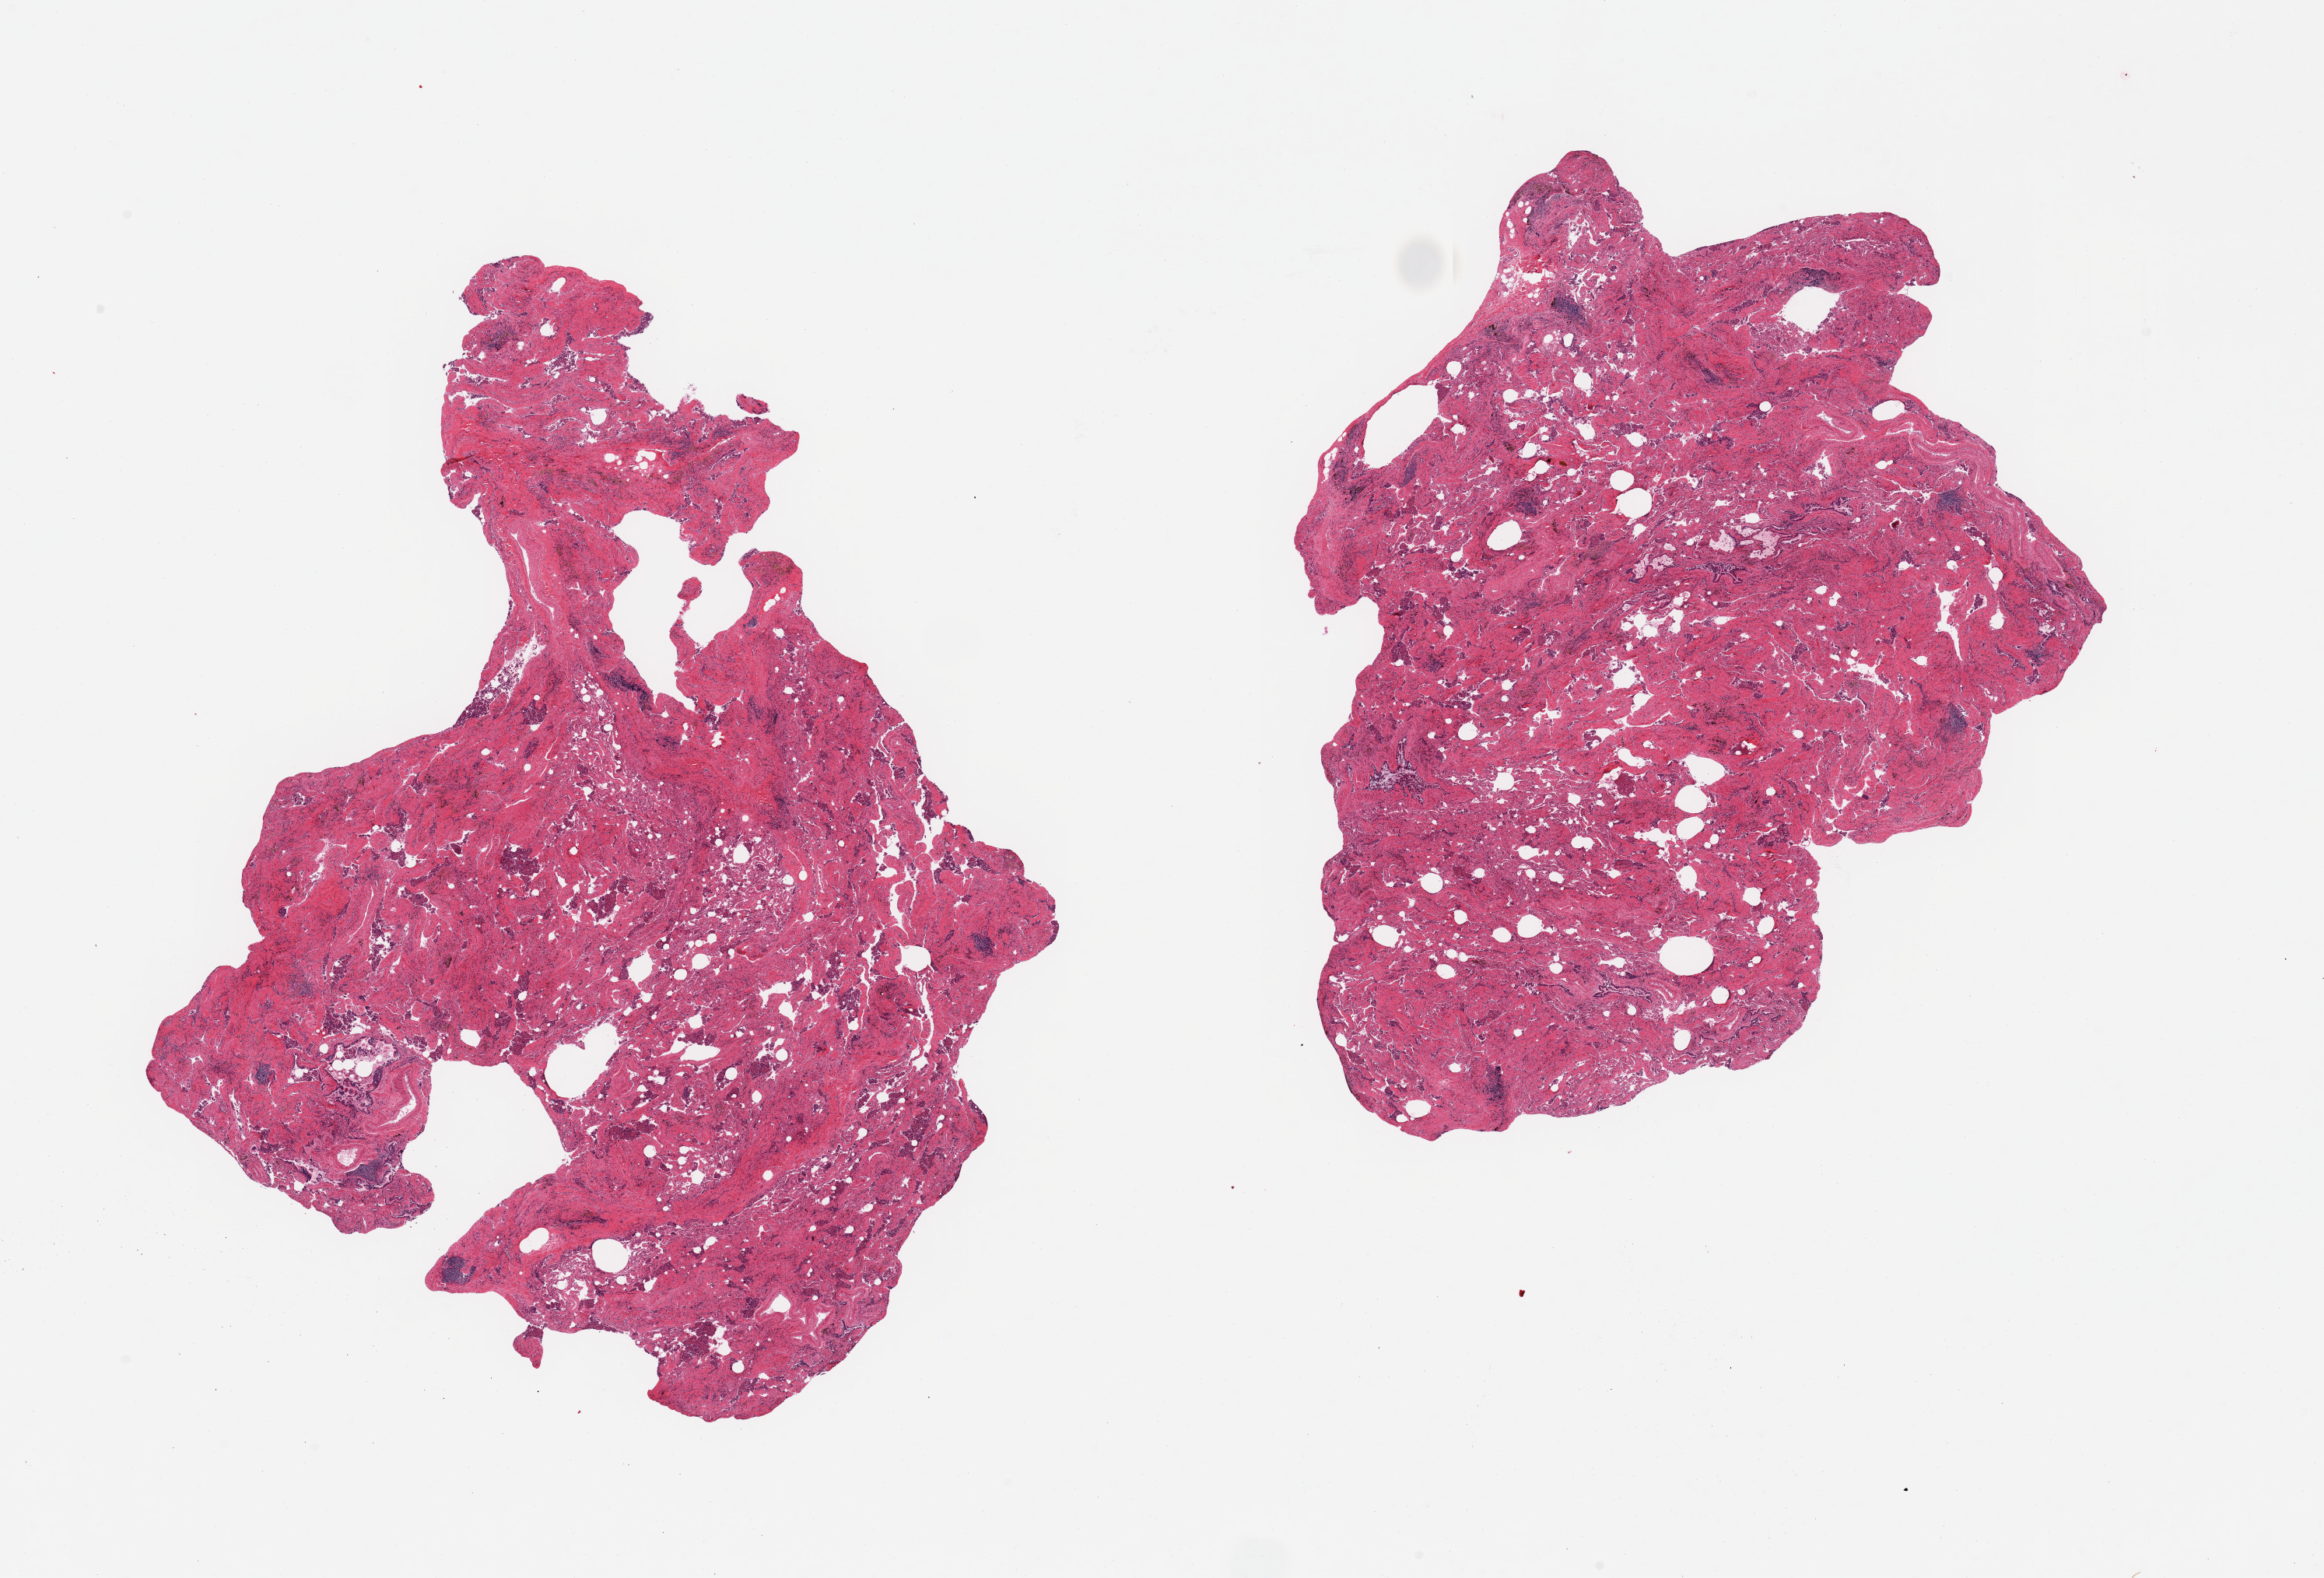
Hematoxylin and eosin (H&E) whole-slide image, a low-resolution overview of the entire scanned area, about 23.6 x 16.0 mm; PAXgene-fixed, paraffin-embedded tissue; sampled site (target tissue): lung; donor tissue sample. Donor: male.
Review note (as recorded): 2 pieces, advanced interstitial fibrosis, end-stage.